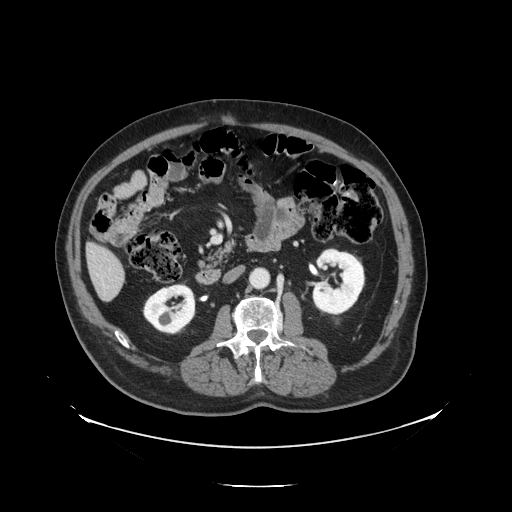
Contrast-enhanced abdominal CT, one axial slice. Slice 42 of 138 in the series (ordered by position). Reconstruction kernel STANDARD. 120 kVp. Soft-tissue window (W 400 / L 40 HU). 2.5 mm slice thickness. 512 × 512 image matrix. Male patient, age 77 years. Case-level facts recorded for this patient, not image findings: diagnosis: colorectal cancer liver metastases, imaged before liver resection; multiple liver metastases: no; largest metastasis: 1.5 cm.
Structures marked on this image (manually delineated by an expert):
- liver: bounding box (x1, y1, x2, y2) in pixels: (88, 245, 125, 301)
- planned liver remnant (the part of the liver to remain after resection): (88, 245, 122, 276)